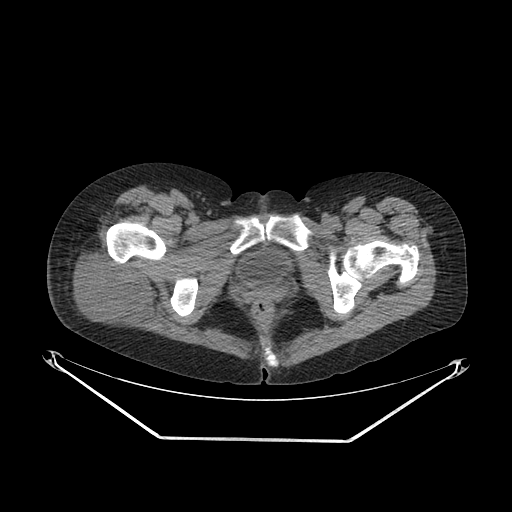
CT of an extremity soft-tissue mass (from a PET/CT study), one axial slice. Slice 43 of 267 in the series (ordered by position). 140 kVp. Soft-tissue window (W 400 / L 40 HU). 512 × 512 image matrix, field of view 500 × 500 mm. Female patient. From the clinical record (not read from this slice): histological type: epithelioid sarcoma with vascular differentiation; site of the primary tumour: right buttock.
Outlined on this slice (expert contour drawn on MRI and transferred to this co-registered scan by the dataset authors):
- gross tumour volume (mass): box from (x=66, y=244) to (x=156, y=330) px